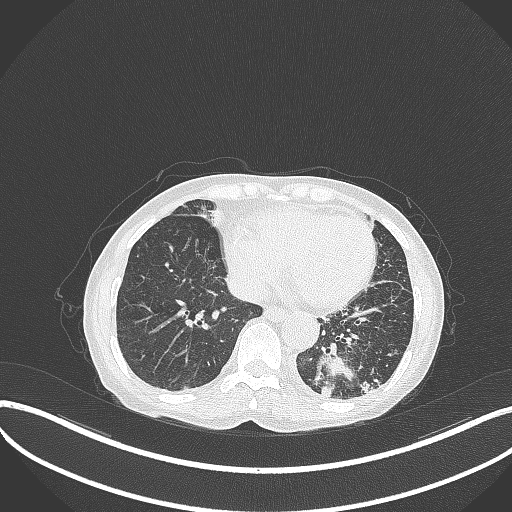
Chest CT, one axial slice. Slice 89 of 370 in the series (ordered by position). Reconstruction kernel B70f. 120 kVp. Lung window (W 1500 / L -600 HU). 1 mm slice thickness. 512 × 512 image matrix. Patient: female, 78 years. From the clinical record (not read from this slice): clinical TNM (as recorded): T3 N0 M1.
Annotated regions visible in this slice (rectangle marked by the reading radiologist):
- lung tumour (recorded histology: squamous cell carcinoma): bounding box <314,343,356,401> (left, top, right, bottom; pixels)